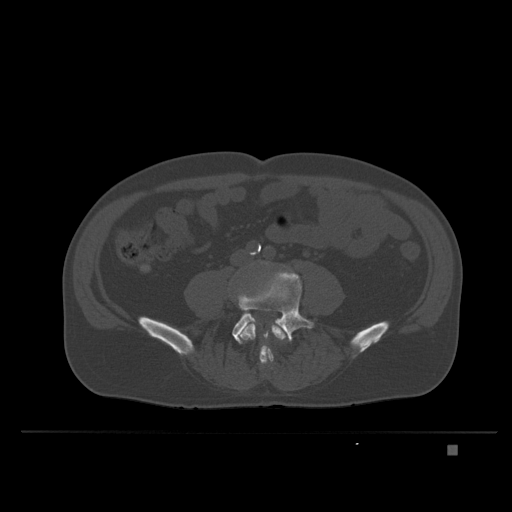
CT including the spine, one axial slice. Slice 64 of 435 in the series (ordered by position). Bone window (W 1800 / L 400 HU). 1.5 mm slice thickness. 512 × 512 image matrix, field of view 434 × 434 mm. Male patient, age 73 years. From the clinical record (not read from this slice): primary cancer: skin.
Annotated regions visible in this slice (semi-automatically segmented with operator editing):
- L4 vertebra: box from (x=238, y=317) to (x=288, y=369) px
- L5 vertebra: (x=232, y=272)–(x=314, y=344)